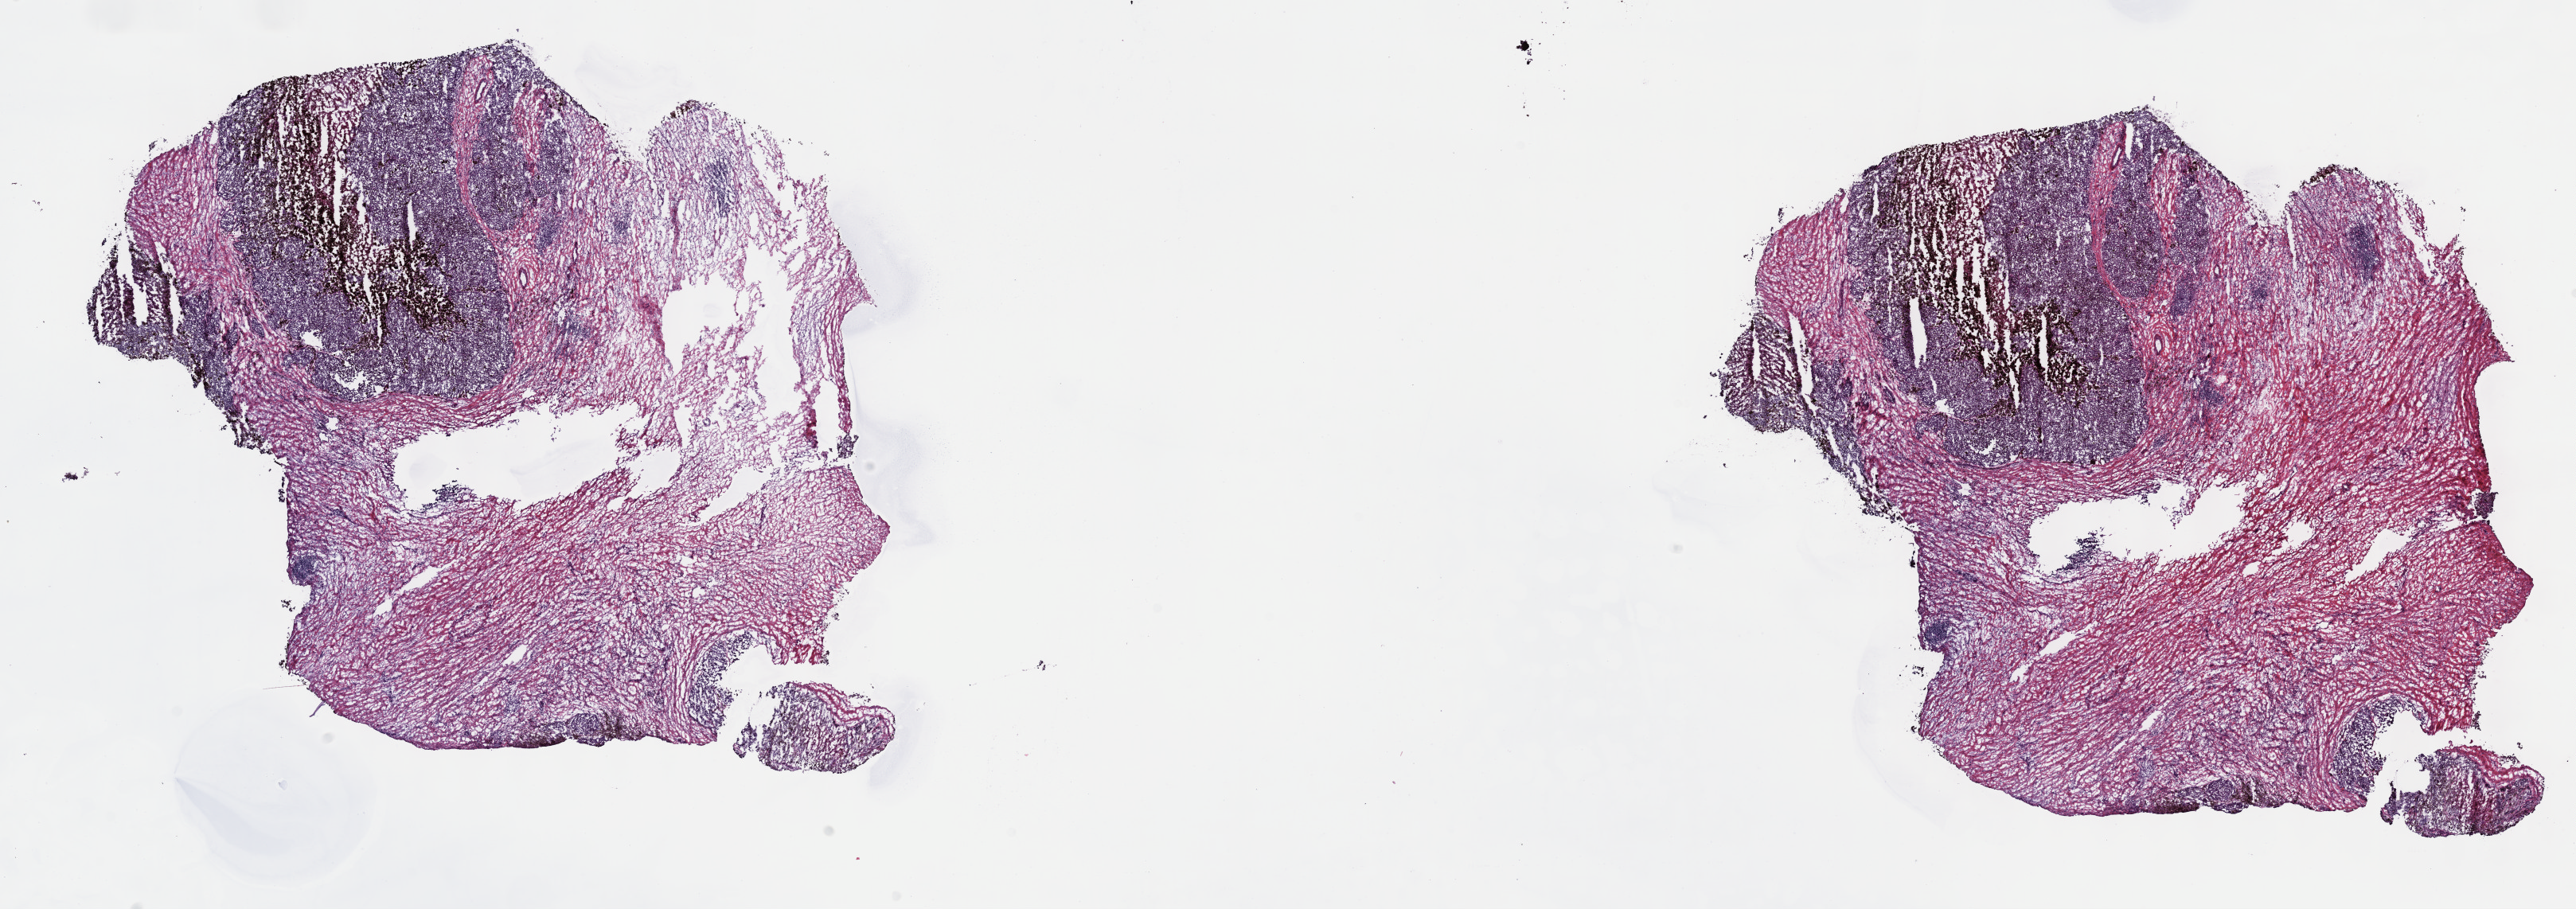
Hematoxylin and eosin (H&E) stained whole-slide image, a low-resolution overview of the entire scanned area, about 26.2 x 9.2 mm (acquisition: 40x scan); frozen section from the top of the tissue portion; metastatic tumour sample, sampled site: lymph nodes of inguinal region or leg. Male, age 37 years at initial diagnosis. Pathologist review of this section (percent, as recorded): tumour cells 50%, tumour nuclei 60%, normal cells 0%, stromal cells 50%, necrosis 0%. Infiltration values recorded for this section: lymphocyte infiltration 0%, monocyte infiltration 0%, neutrophil infiltration 0%.
This section: metastatic tumour tissue. Patient diagnosis: Superficial spreading melanoma.